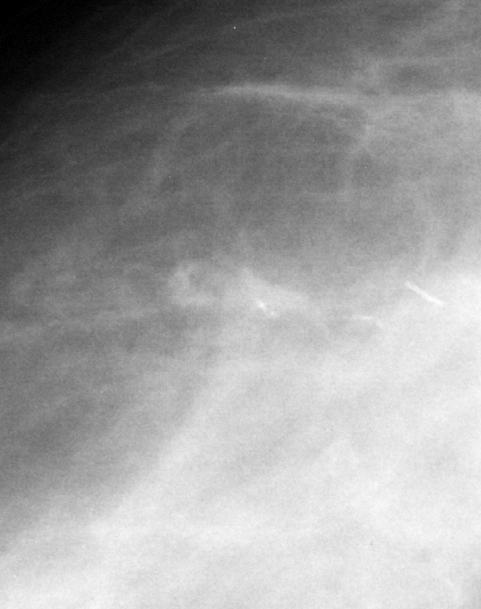
Region of interest cut from a scanned film mammogram (one marked finding); right breast; CC view; BI-RADS breast density category 2 (scale 1–4).
Calcifications, morphology fine linear branching, distribution linear; BI-RADS assessment category 4; pathology result (as recorded, not read from the image): benign.